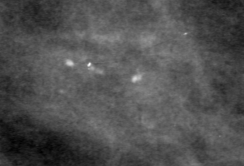
Crop from a digitized film mammogram around one marked abnormality, left breast, CC view, BI-RADS breast density category 4 (scale 1–4).
Calcifications, morphology pleomorphic, distribution clustered; BI-RADS assessment category 4; subtlety rating 2 on a 1 (subtle) to 5 (obvious) scale; pathology result (as recorded, not read from the image): benign.